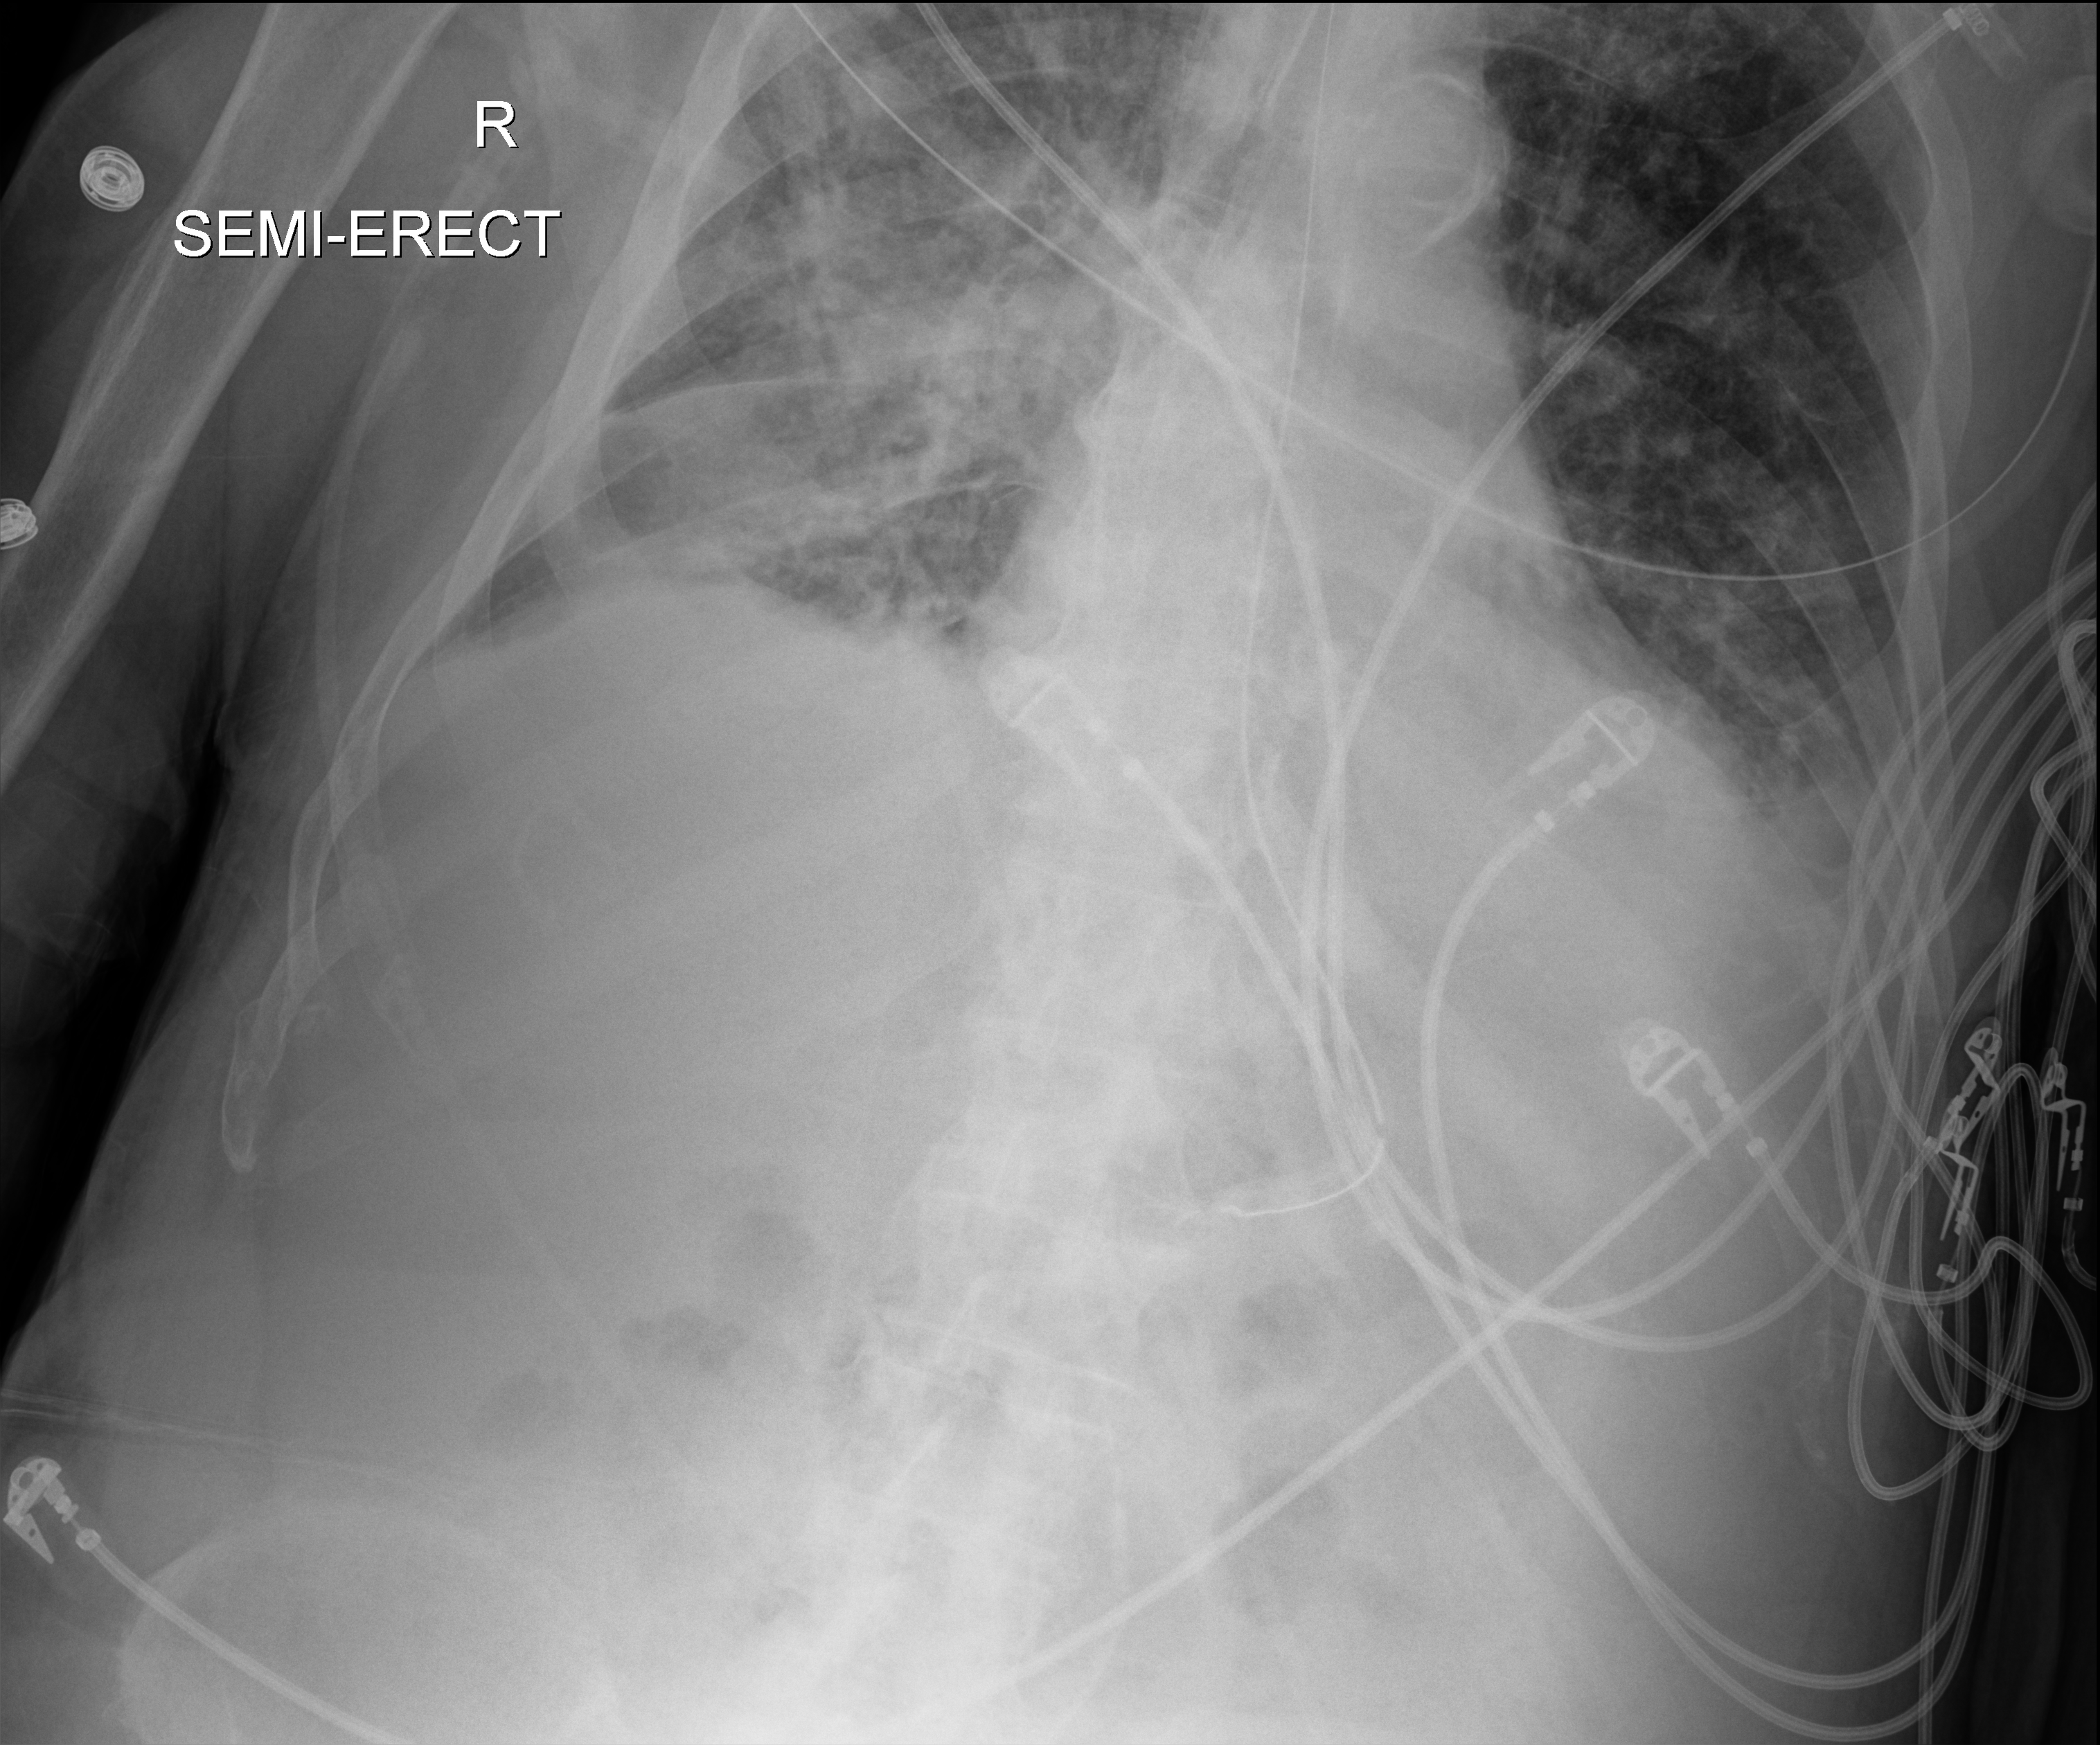
Bedside chest radiograph (digital radiography), anteroposterior (AP) projection. Male patient hospitalised with COVID-19, age 75–90 years.
Hospital-stay facts (about this admission, not read from this image; timing relative to this image not recorded): diabetes (admission record): yes; mechanically ventilated during this hospital stay: yes.